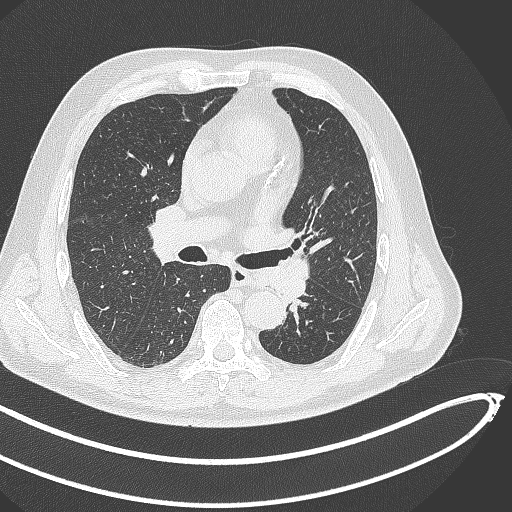
Chest CT, one axial slice. Position 265 of 468 along the scan axis. Reconstruction kernel B70f. Lung window (W 1500 / L -600 HU). 1 mm slice thickness. 512 × 512 image matrix, field of view 400 × 400 mm. Patient: male, 64 years. From the clinical record (not read from this slice): clinical TNM (as recorded): T1c N0 M0.
Annotated regions visible in this slice (rectangle marked by the reading radiologist):
- lung tumour (recorded histology: squamous cell carcinoma): bounding box (x1, y1, x2, y2) in pixels: (266, 253, 316, 303)